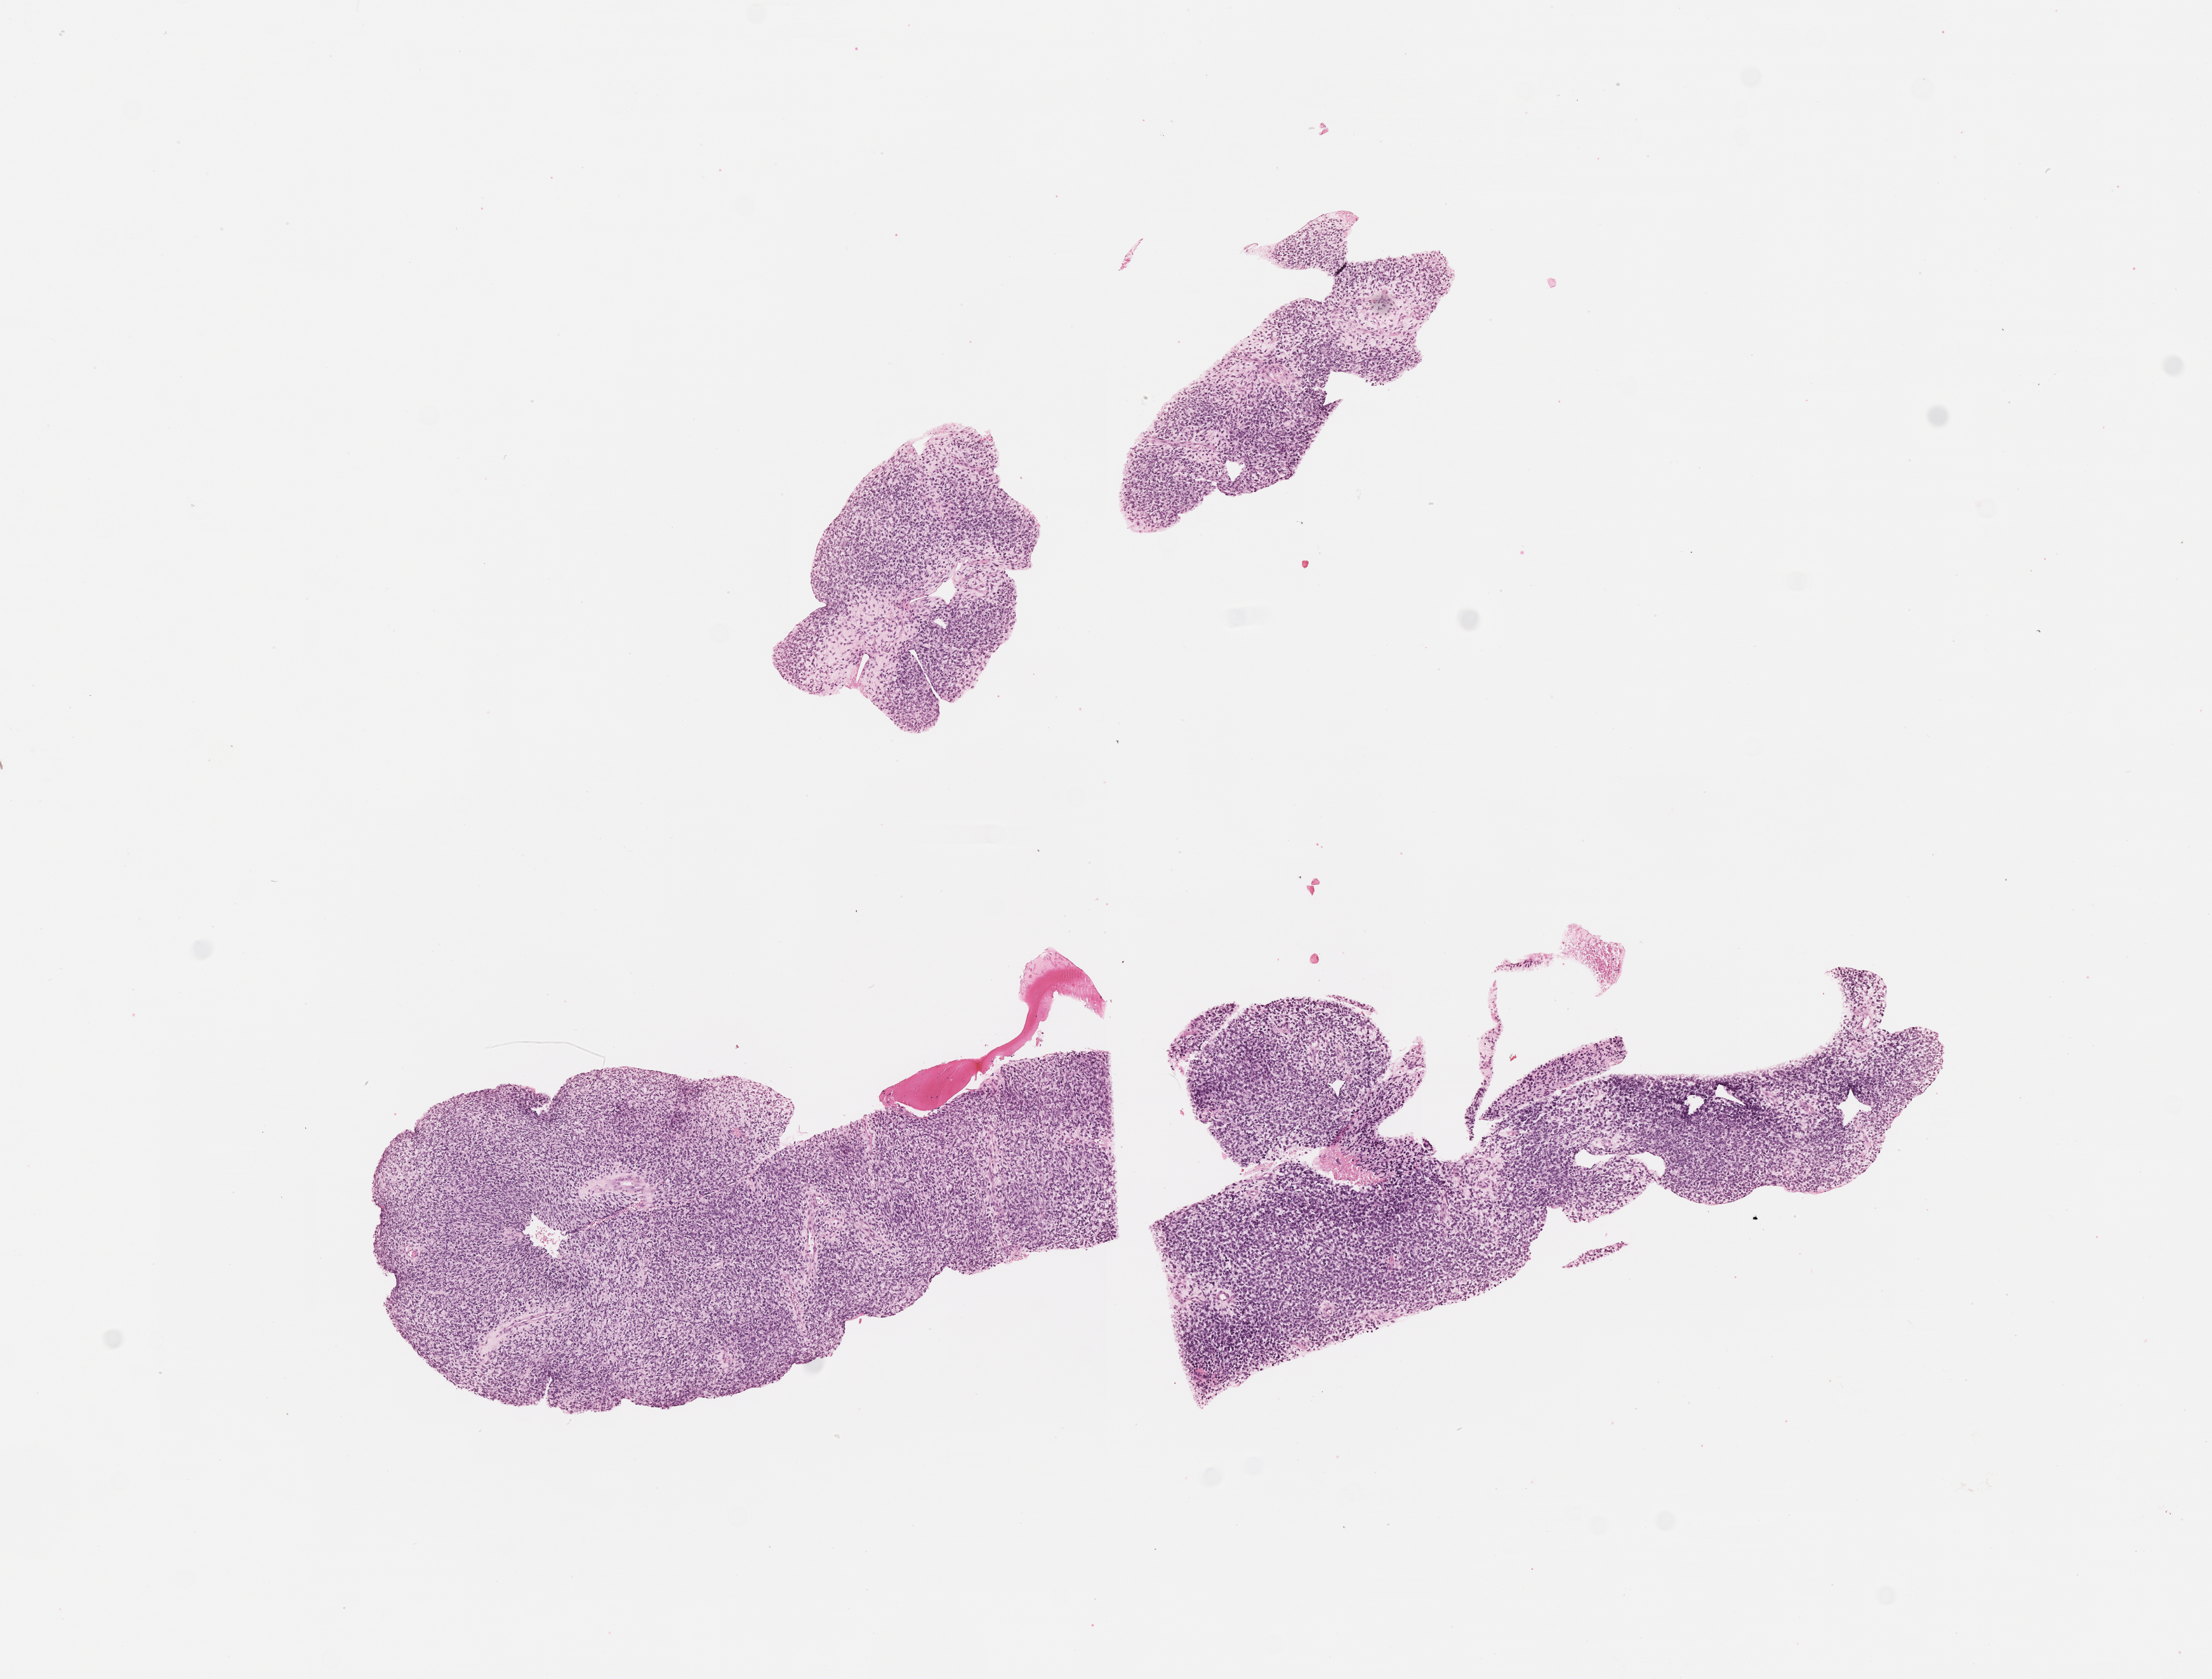
Haematoxylin and eosin whole-slide image of tumor tissue — whole scanned area (about 7.0 x 5.3 mm) shown as a low-resolution overview. Formalin-fixed paraffin-embedded section. Site: pelvis (prostate). Male patient, age at diagnosis 1.2 years.
Stage (as recorded): 3. Diagnosis: rhabdomyosarcoma; histological classification: embryonal rhabdomyosarcoma.